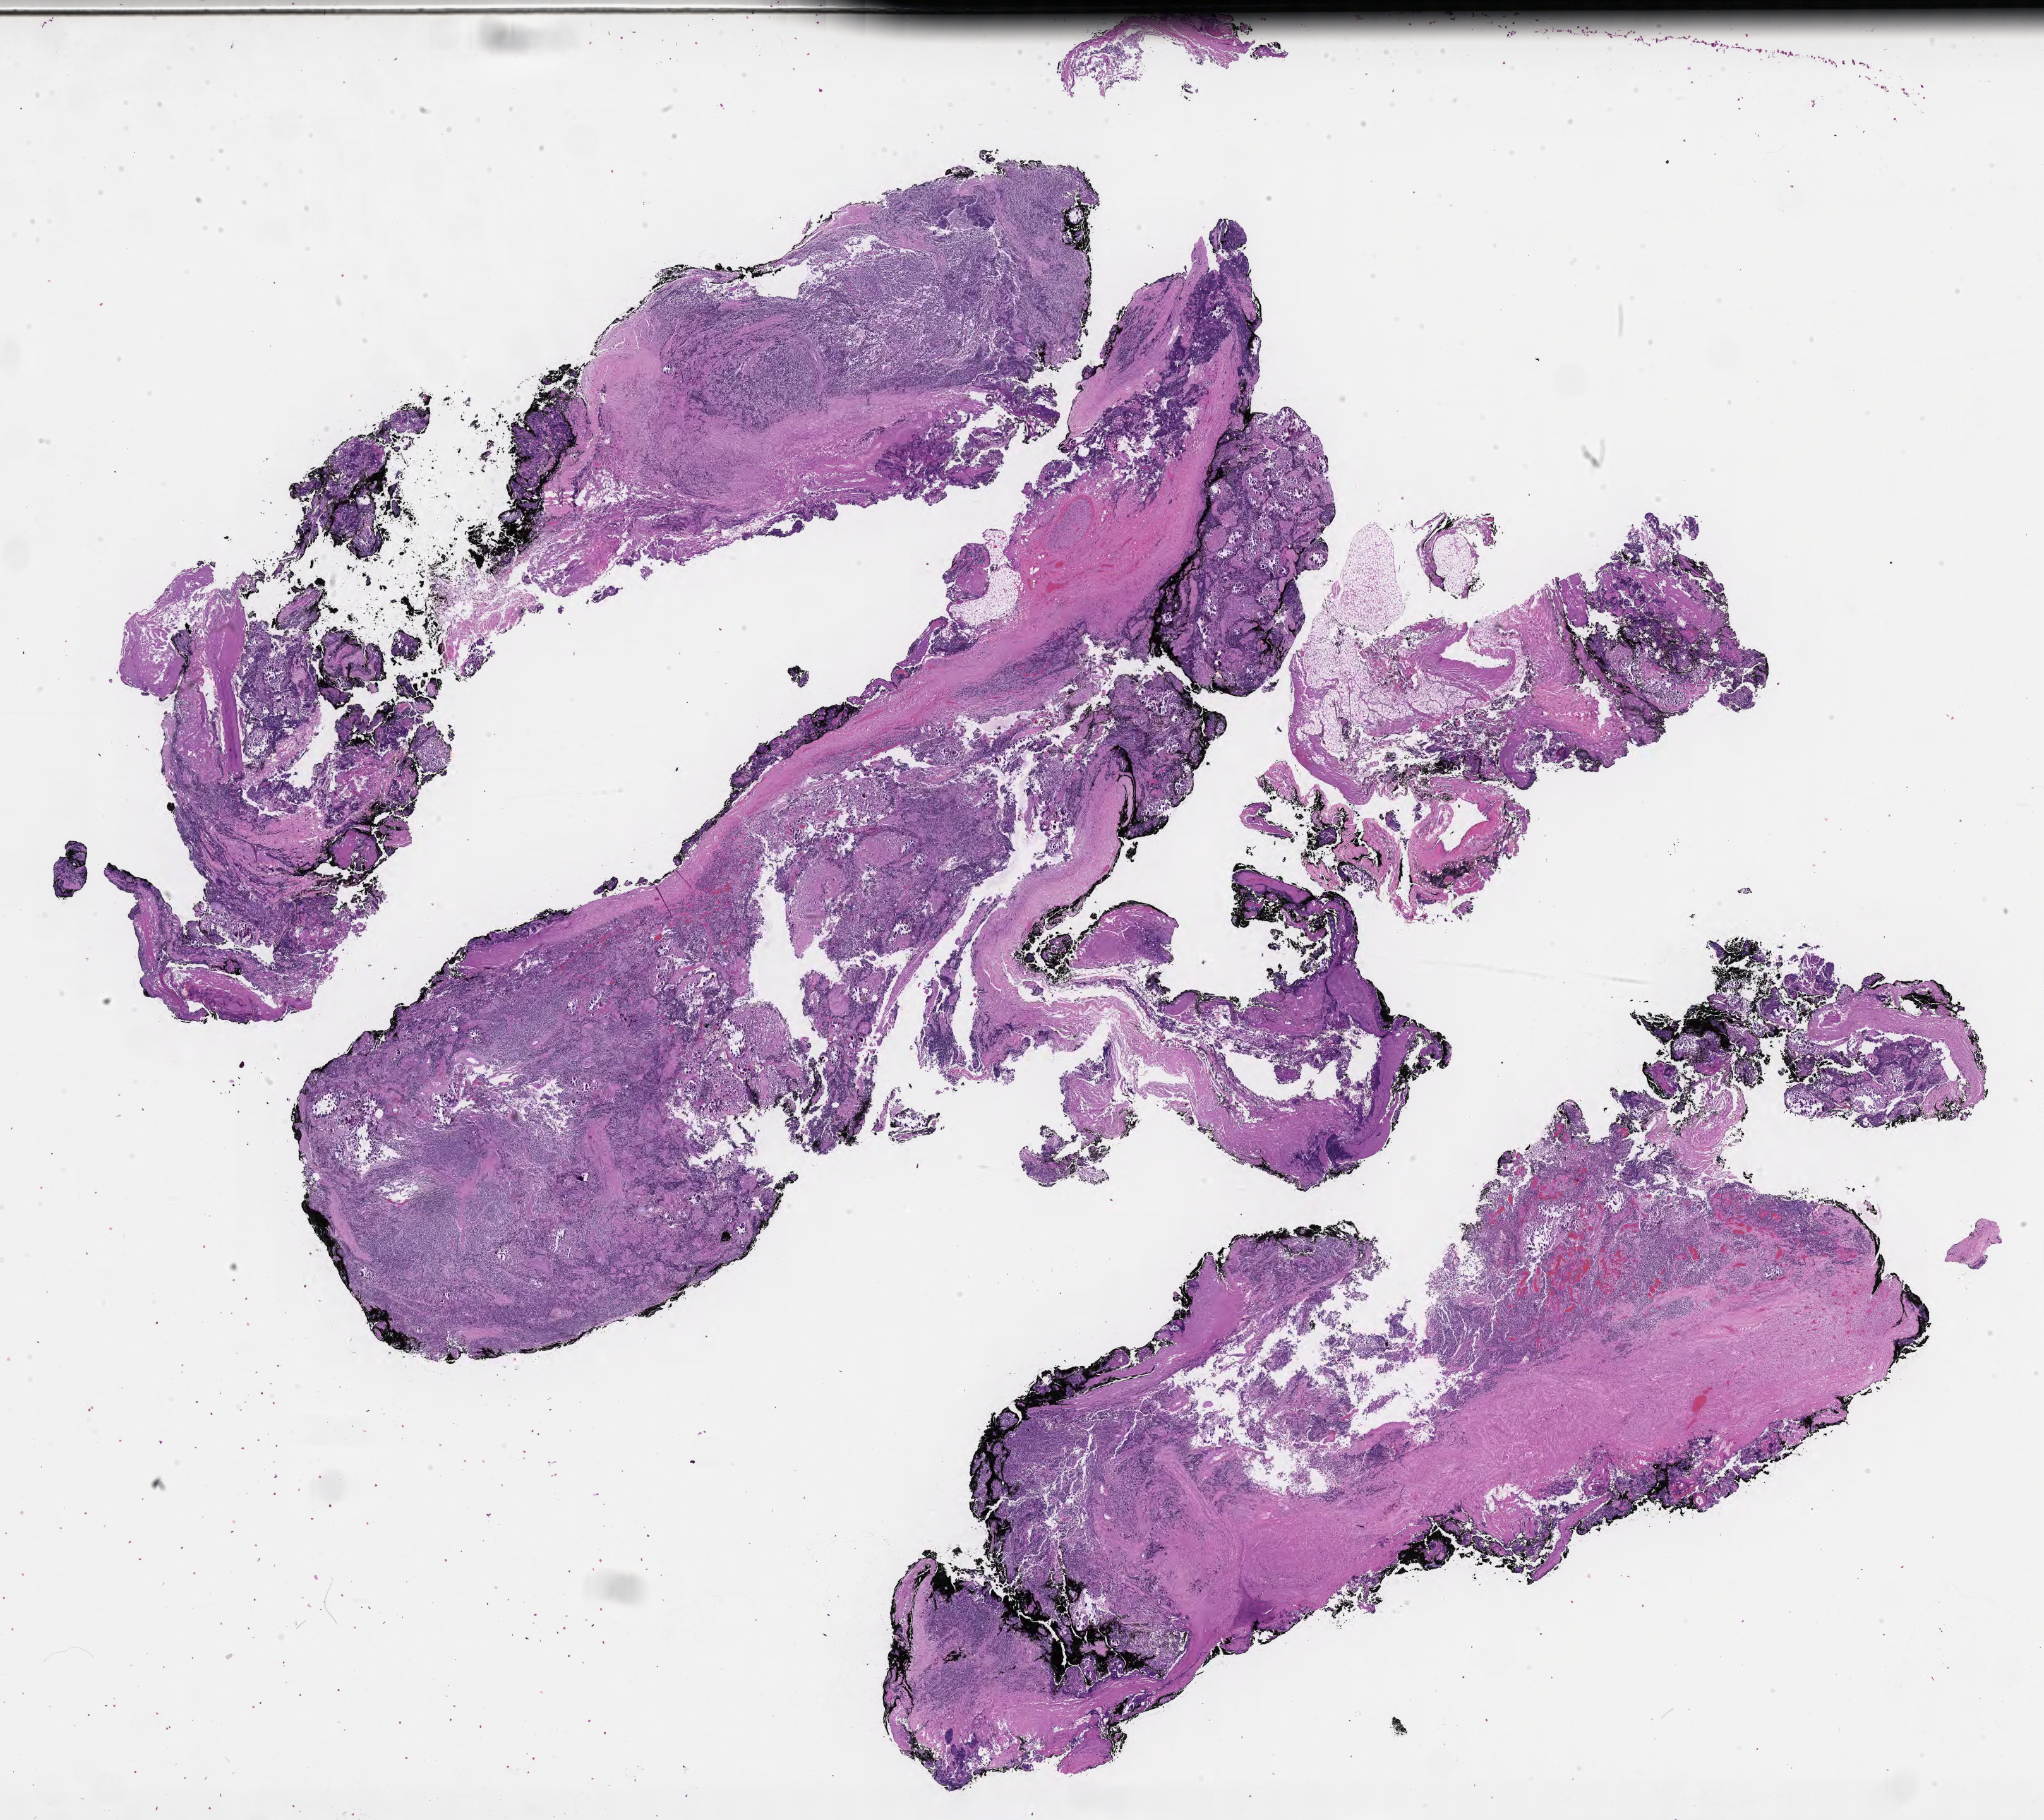
Whole-slide image, haematoxylin and eosin stain of tumor tissue from the soft tissue — whole scanned area (about 26.2 x 23.3 mm) shown as a low-resolution overview, formalin-fixed, paraffin-embedded (FFPE) tissue. Male patient, age 410 days.
- diagnosis: Neuroblastoma, NOS